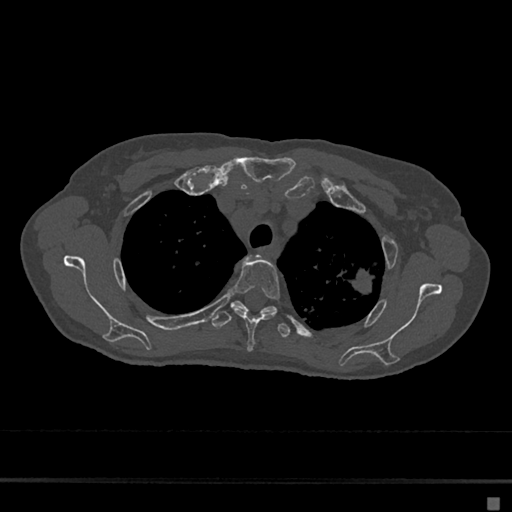
CT including the spine, one axial slice; position 529 of 797 along the scan axis; reconstruction kernel Br40s/3; 120 kVp; bone window (W 1800 / L 400 HU); 512 × 512 image matrix, field of view 360 × 360 mm. Patient: female, 68 years. From the clinical record (not read from this slice): primary cancer: renal.
Structures marked on this image (semi-automatically segmented with operator editing):
- T2 vertebra: bounding box [x1, y1, x2, y2] px = [244, 256, 252, 261]
- T3 vertebra: [232, 259, 280, 351]
- T4 vertebra: [211, 301, 291, 338]